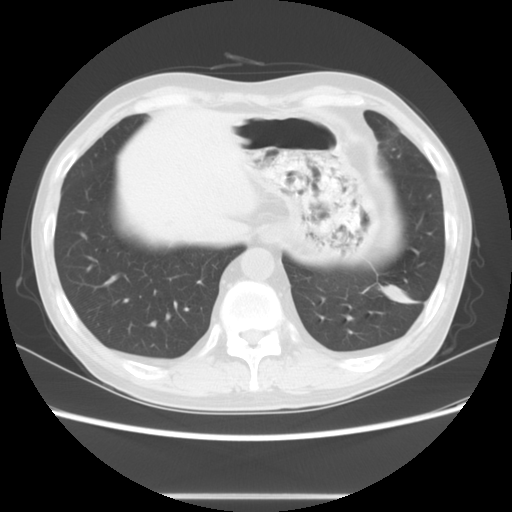
Chest CT, one axial slice. Slice 19 of 63 in the series (ordered by position). Reconstruction kernel STANDARD. Lung window (W 1500 / L -600 HU). 512 × 512 image matrix. Male patient, age 49 years. Case-level facts recorded for this patient, not image findings: clinical TNM (as recorded): T3 N0 M0.
Structures marked on this image (bounding box drawn by a radiologist):
- lung tumour (recorded histology: squamous cell carcinoma): bounding box <377,277,419,318> (left, top, right, bottom; pixels)